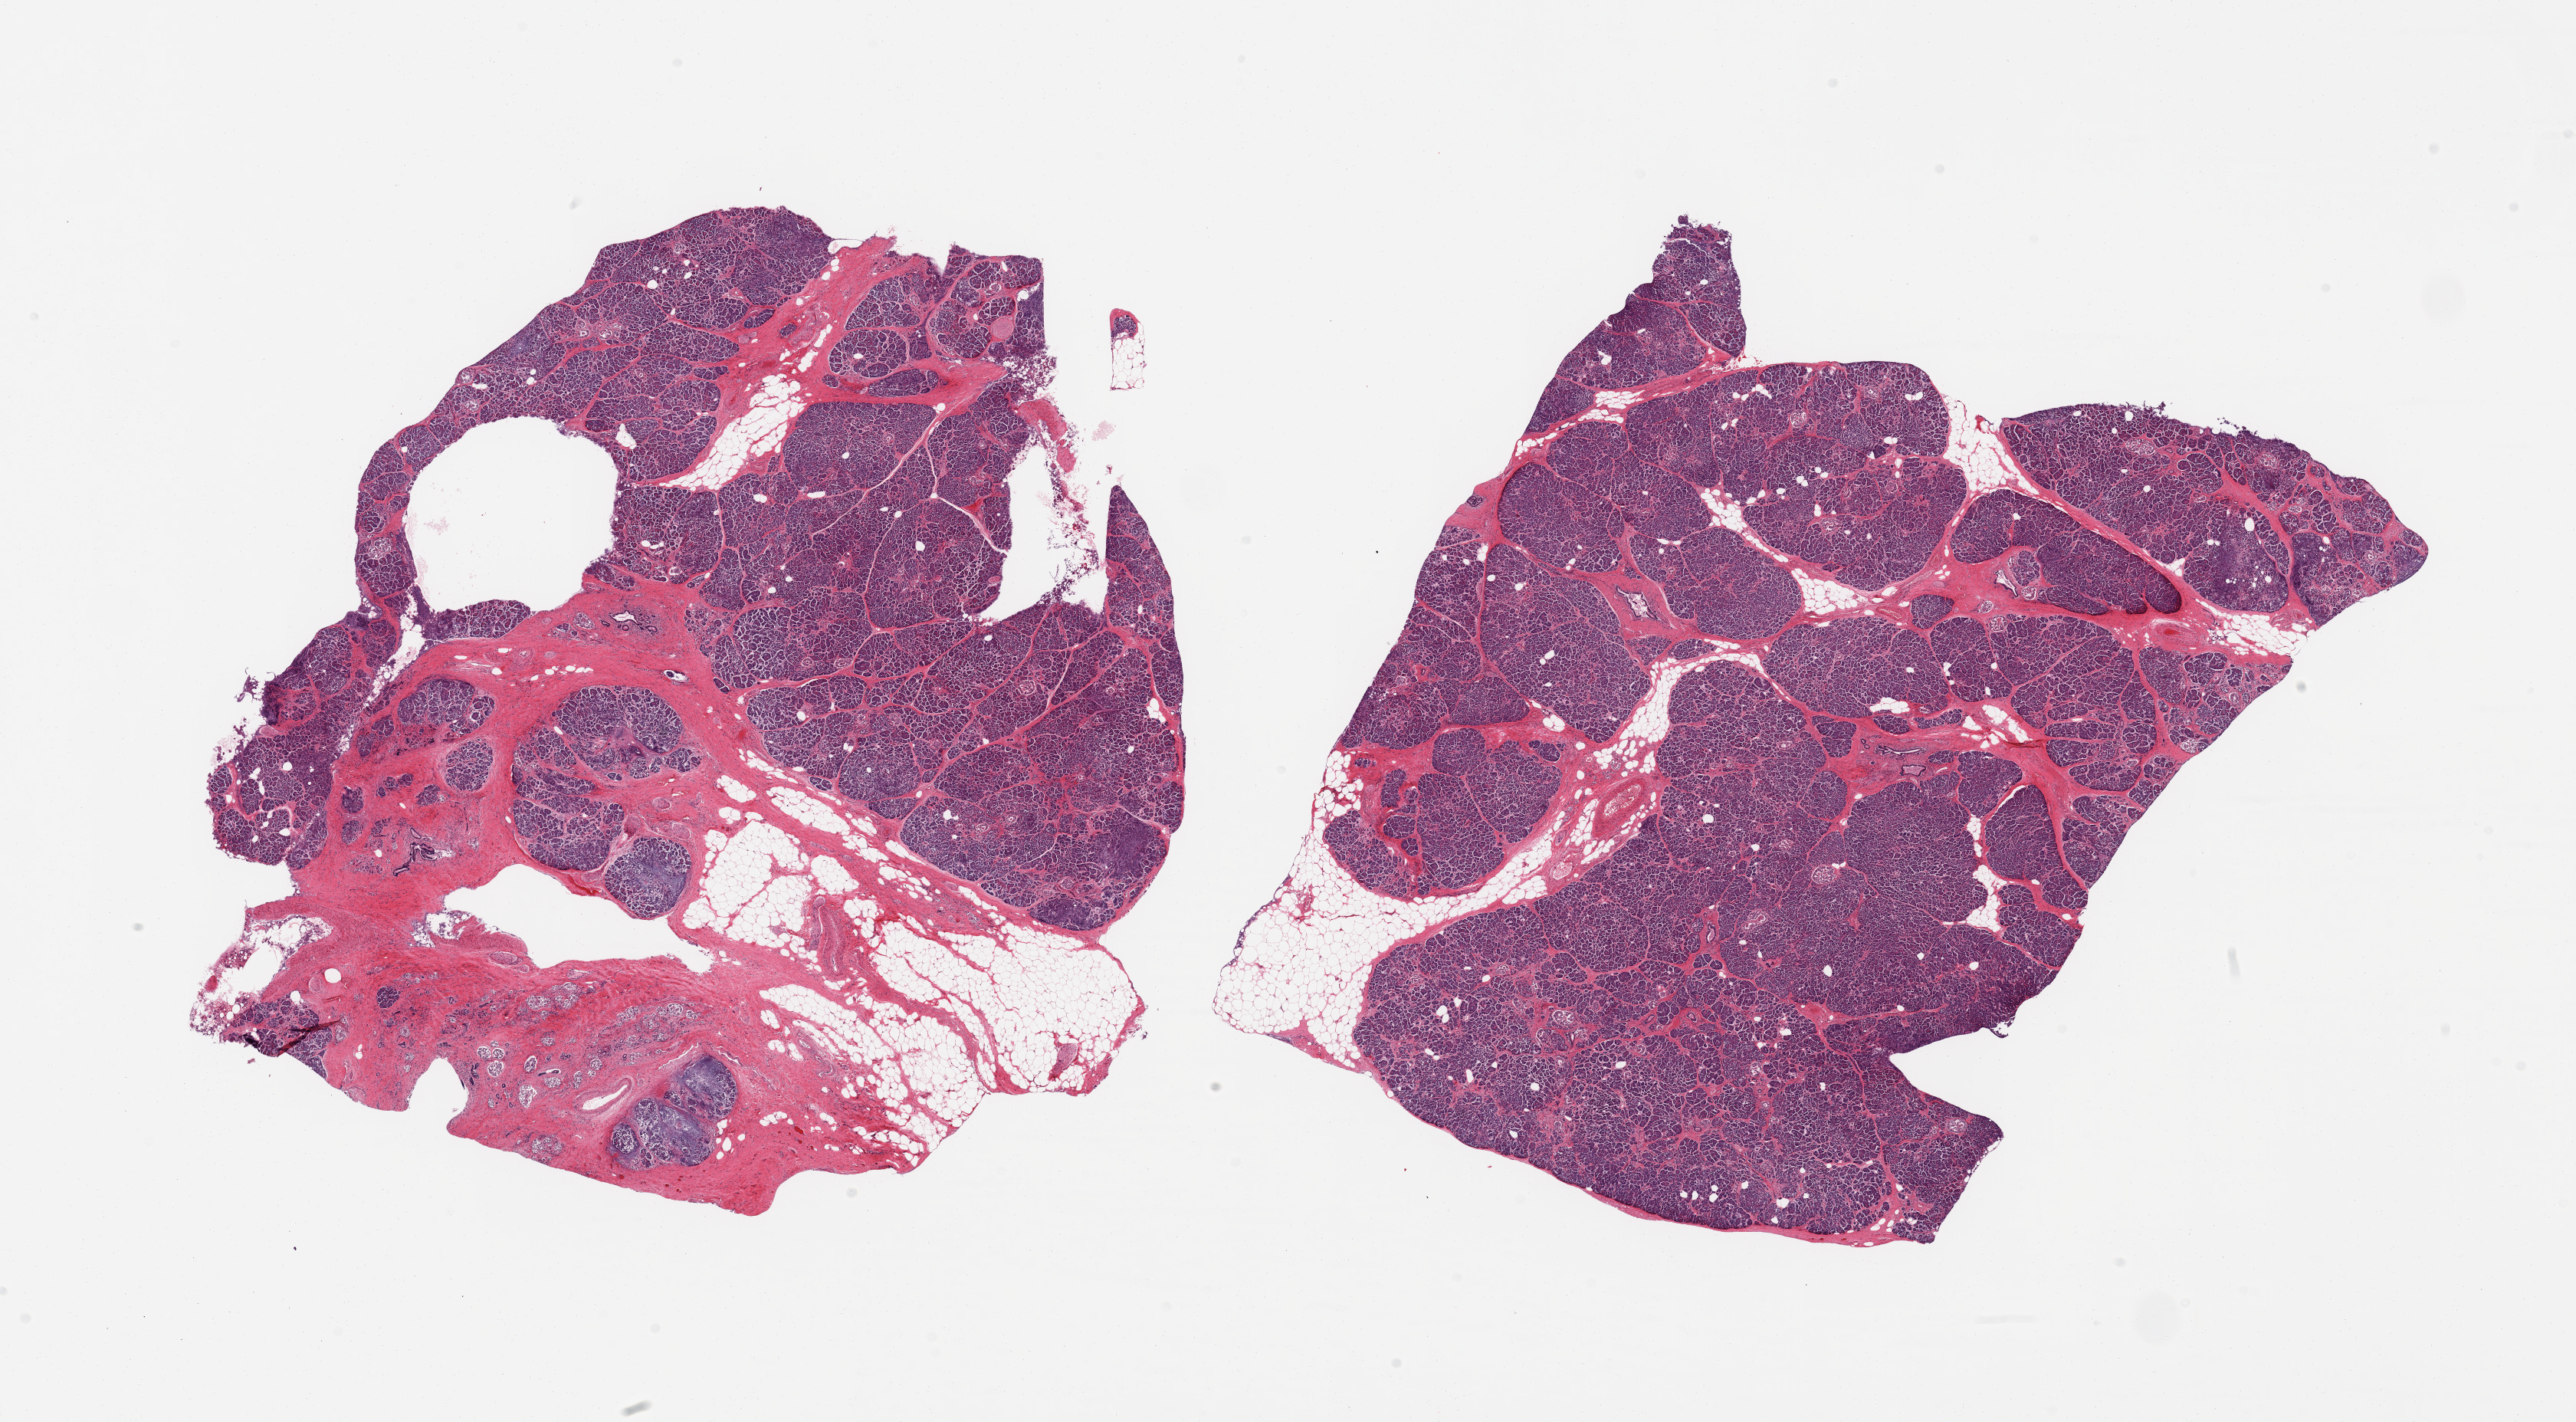
H&E whole-slide image — a low-resolution overview of the entire scanned area, about 26.6 x 14.7 mm, PAXgene-fixed paraffin-embedded (PFPE) section, section of pancreas (target tissue), donor tissue sample. Donor: male.
Review note (as recorded): 2 pieces, moderately advanced saponification; Islets still visible but beginning to degrade.